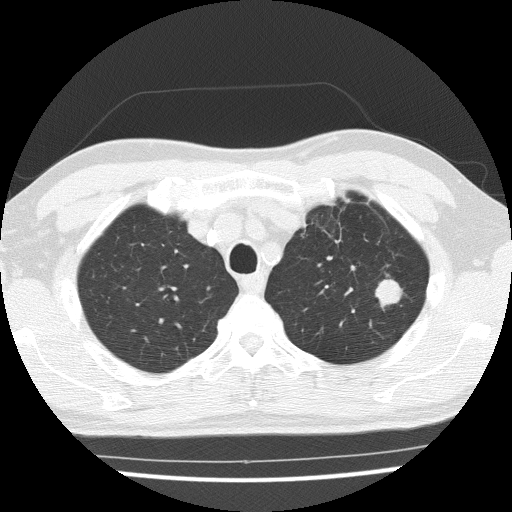
Low-dose screening chest CT, axial slice; third annual screen; lung window (W 1500 / L -600 HU); lung (sharp) reconstruction kernel (FC51). Male participant, aged 65 years at enrolment. Current smoker at enrolment.
- Expert-annotated lung lesion, box from (x=357, y=271) to (x=410, y=317) px.
- Screening reader's record for this exam (one nodule recorded; not confirmed to be the boxed lesion): non-calcified nodule or mass ≥4 mm, left upper lobe, 16 × 15 mm, poorly defined margins, soft tissue attenuation, pre-existing on the prior screen: yes; interval growth: yes.
- Official screen result: positive, other.
- Later outcome: lung cancer diagnosed 42 days after this screen — squamous cell carcinoma, NOS, left upper lobe, moderately differentiated (G2), stage IA (AJCC 6th edition), 25 mm at pathology.